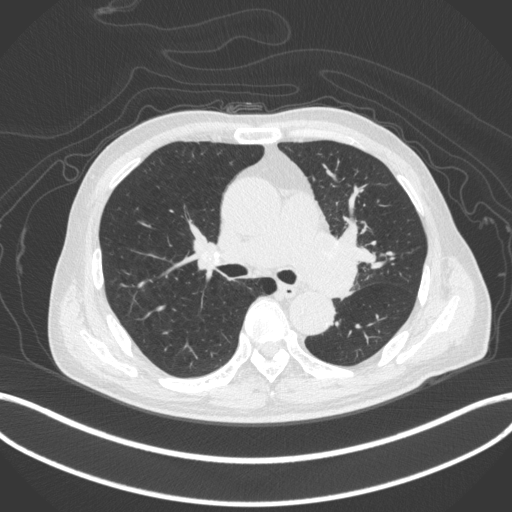
Chest CT, one axial slice. Position 265 of 420 along the scan axis. Lung window (W 1500 / L -600 HU). 512 × 512 image matrix. Patient: male, 77 years. Case-level facts recorded for this patient, not image findings: clinical TNM (as recorded): T3 N1 M0.
Structures marked on this image (rectangle marked by the reading radiologist):
- lung tumour (recorded histology: adenocarcinoma): bounding box [x1, y1, x2, y2] px = [297, 236, 362, 303]